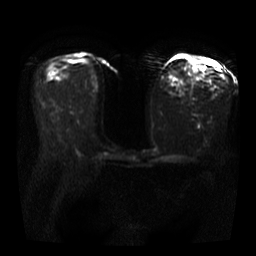
Breast MRI, one axial slice. Slice 19 of 40 in the series (ordered by position). Diffusion-weighted series; image 2 of 4 stored at this slice position (different b-values; order by instance number). 3 T. 5 mm slice thickness. 256 × 256 image matrix, field of view 360 × 360 mm. Female patient.
Annotated regions visible in this slice (expert manual segmentation):
- tumour on diffusion-weighted imaging: bounding box (x1, y1, x2, y2) in pixels: (192, 66, 197, 73)